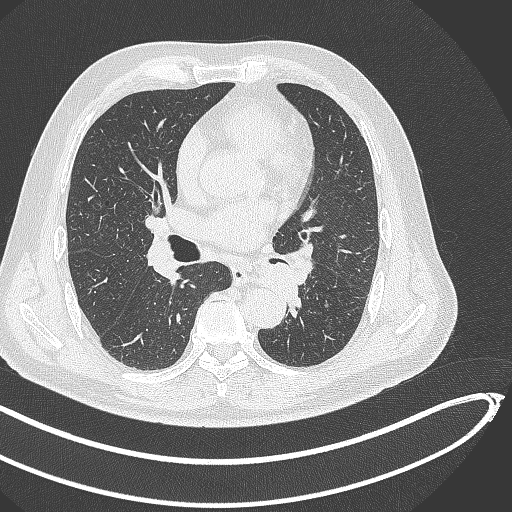
Chest CT, one axial slice. Slice 249 of 468 in the series (ordered by position). Reconstruction kernel B70f. Lung window (W 1500 / L -600 HU). 1 mm slice thickness. 512 × 512 image matrix, field of view 400 × 400 mm. Male patient, age 64 years. Case-level facts recorded for this patient, not image findings: clinical TNM (as recorded): T1c N0 M0; histopathological grade: G2.
Outlined on this slice (rectangle marked by the reading radiologist):
- lung tumour (recorded histology: squamous cell carcinoma): bounding box <252,256,312,314> (left, top, right, bottom; pixels)